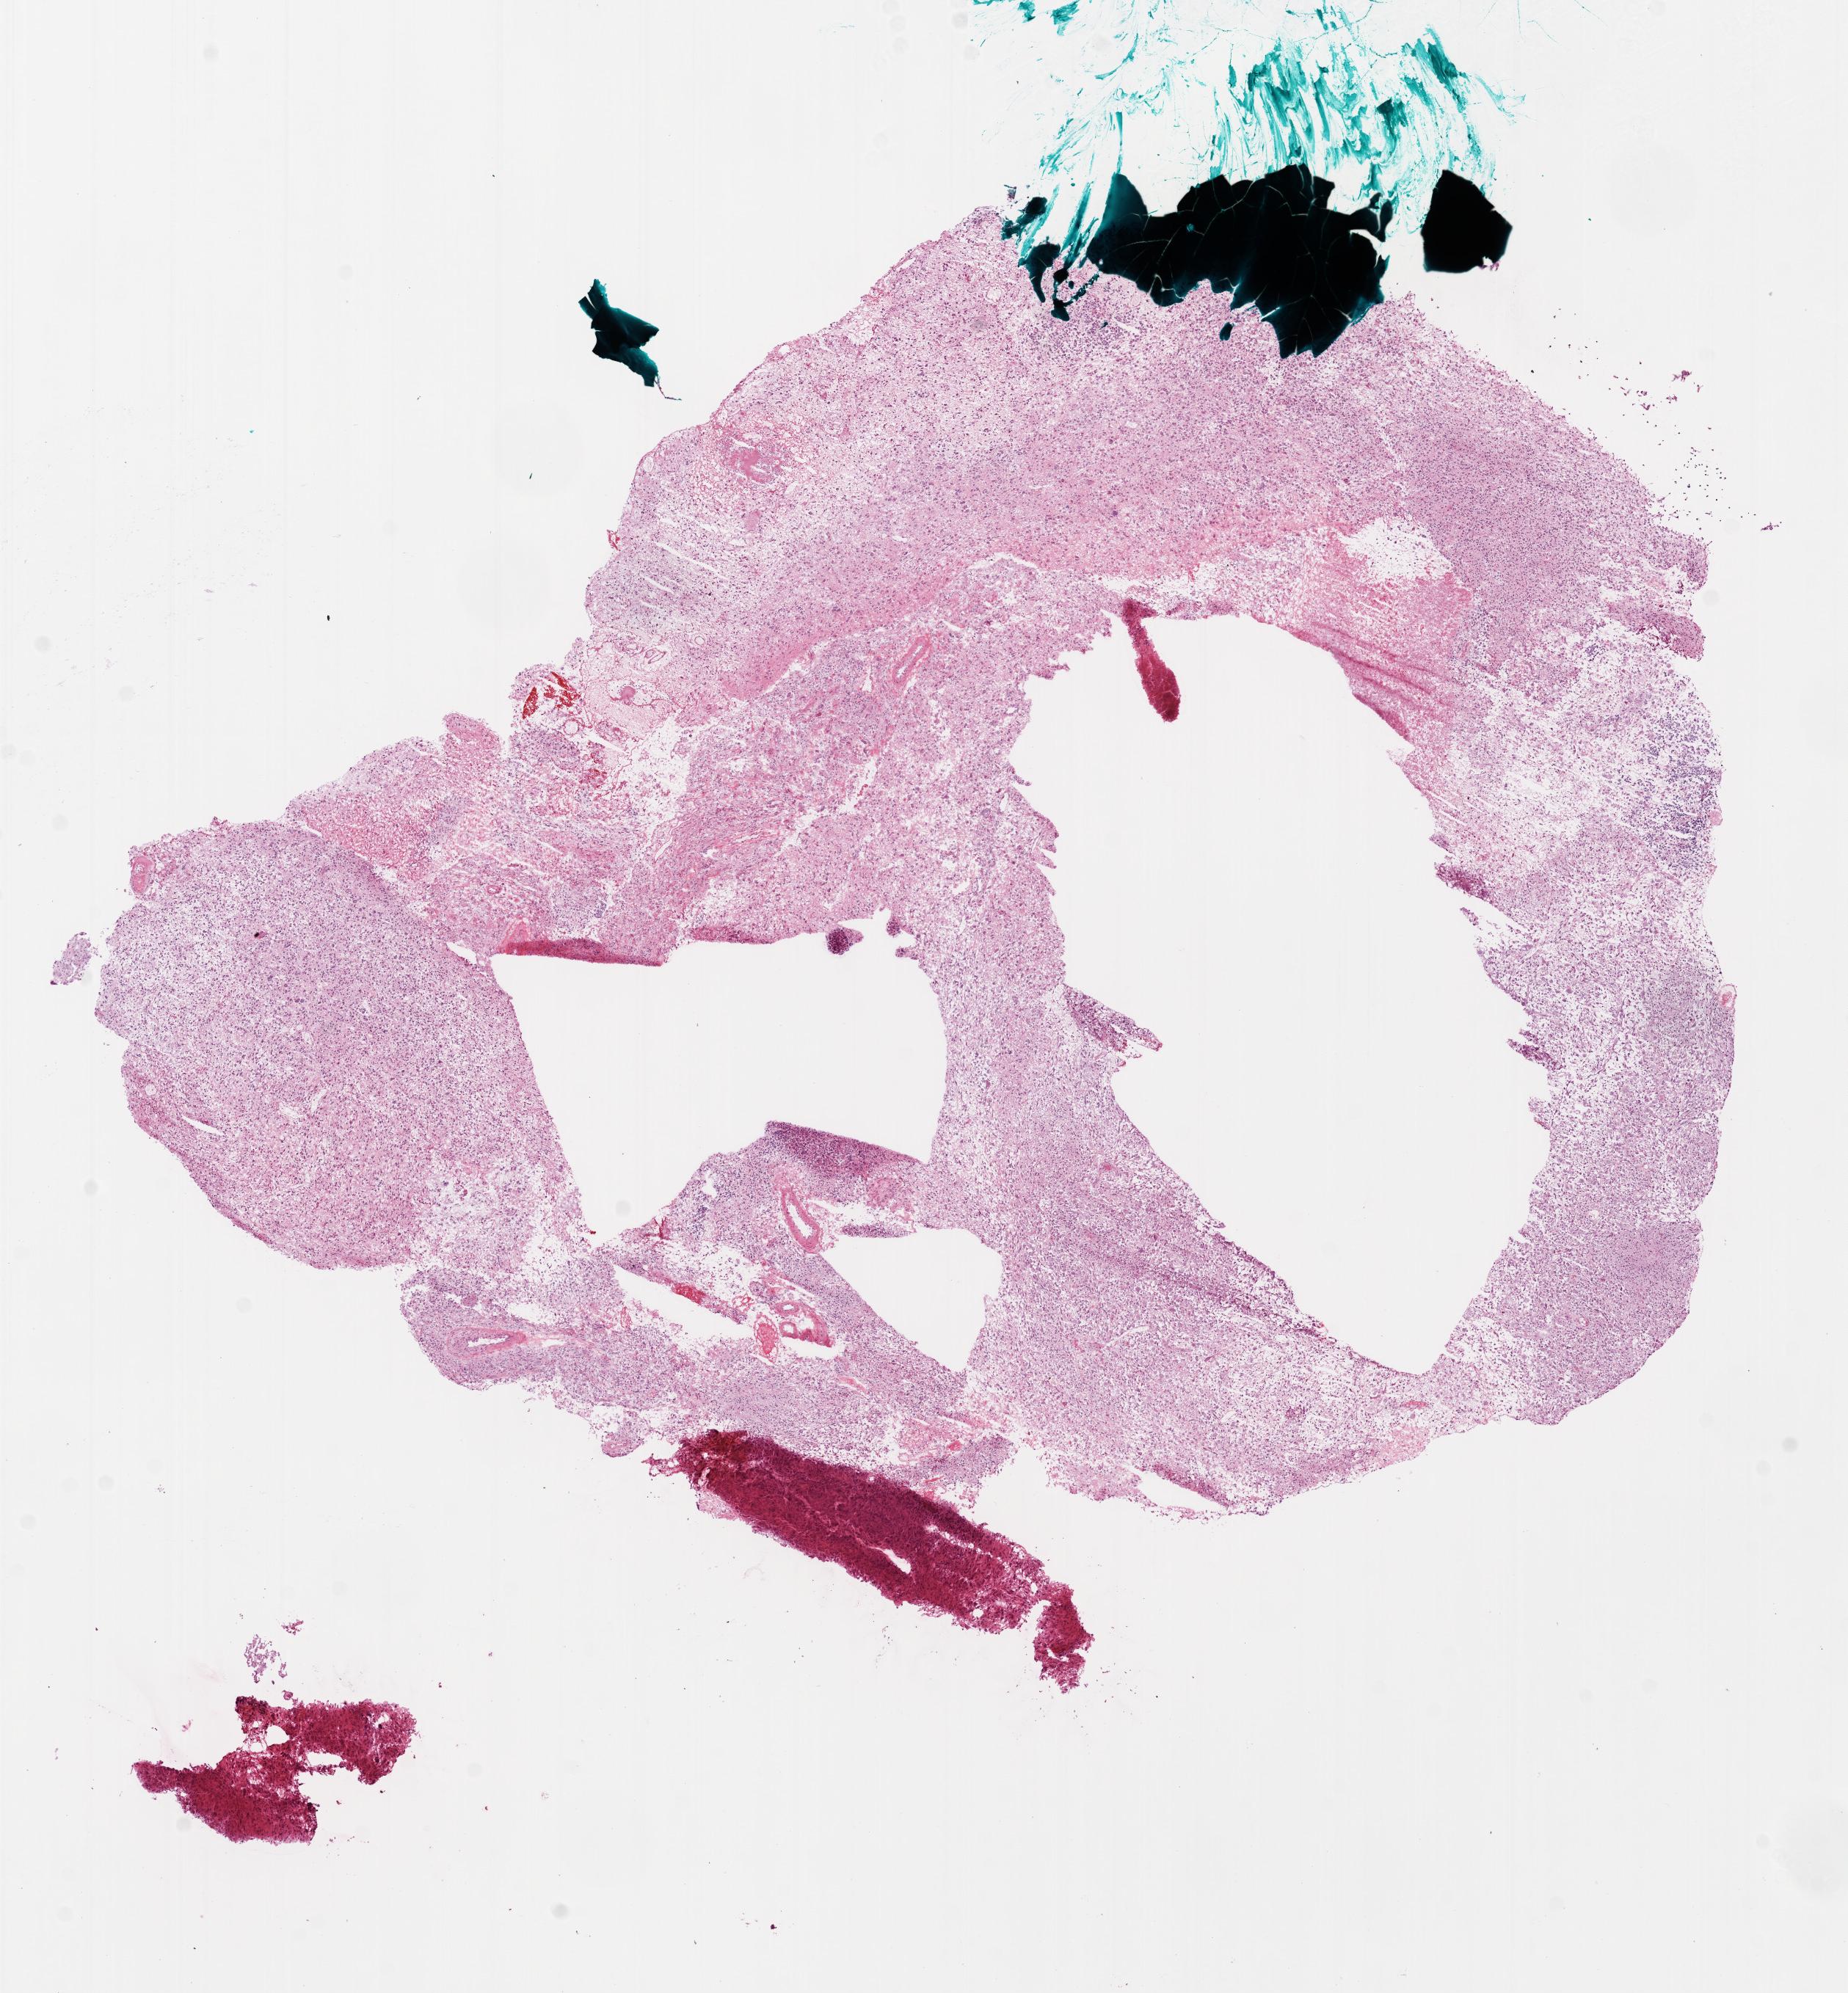
Hematoxylin and eosin (H&E) stained whole-slide image — a low-resolution overview of the entire scanned area, about 10.2 x 11.0 mm. Frozen section from the bottom of the tissue portion. Primary tumour sample from the brain. Patient: male, age at initial diagnosis 60 years. Slide review estimates, as recorded: tumour cells 90%, tumour nuclei 100%.
Diagnosis: Glioblastoma.